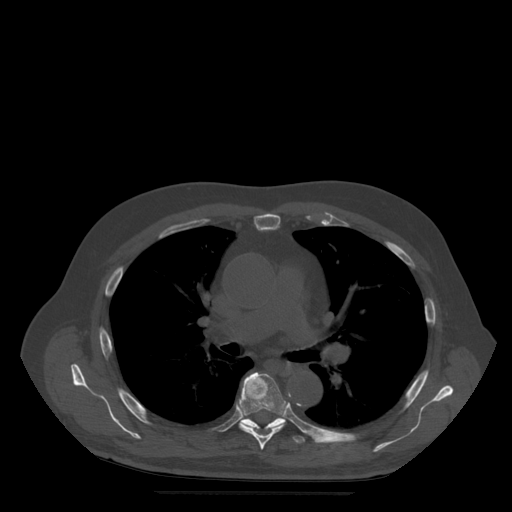
CT including the spine, one axial slice; position 347 of 522 along the scan axis; bone window (W 1800 / L 400 HU); 512 × 512 image matrix, field of view 420 × 420 mm. Patient age 72 years. Case-level facts recorded for this patient, not image findings: primary cancer: prostate.
Outlined on this slice (semi-automatic segmentation, software-assisted and operator-edited):
- T6 vertebra: box from (x=239, y=372) to (x=287, y=450) px
- T7 vertebra: (x=242, y=418)–(x=305, y=444)